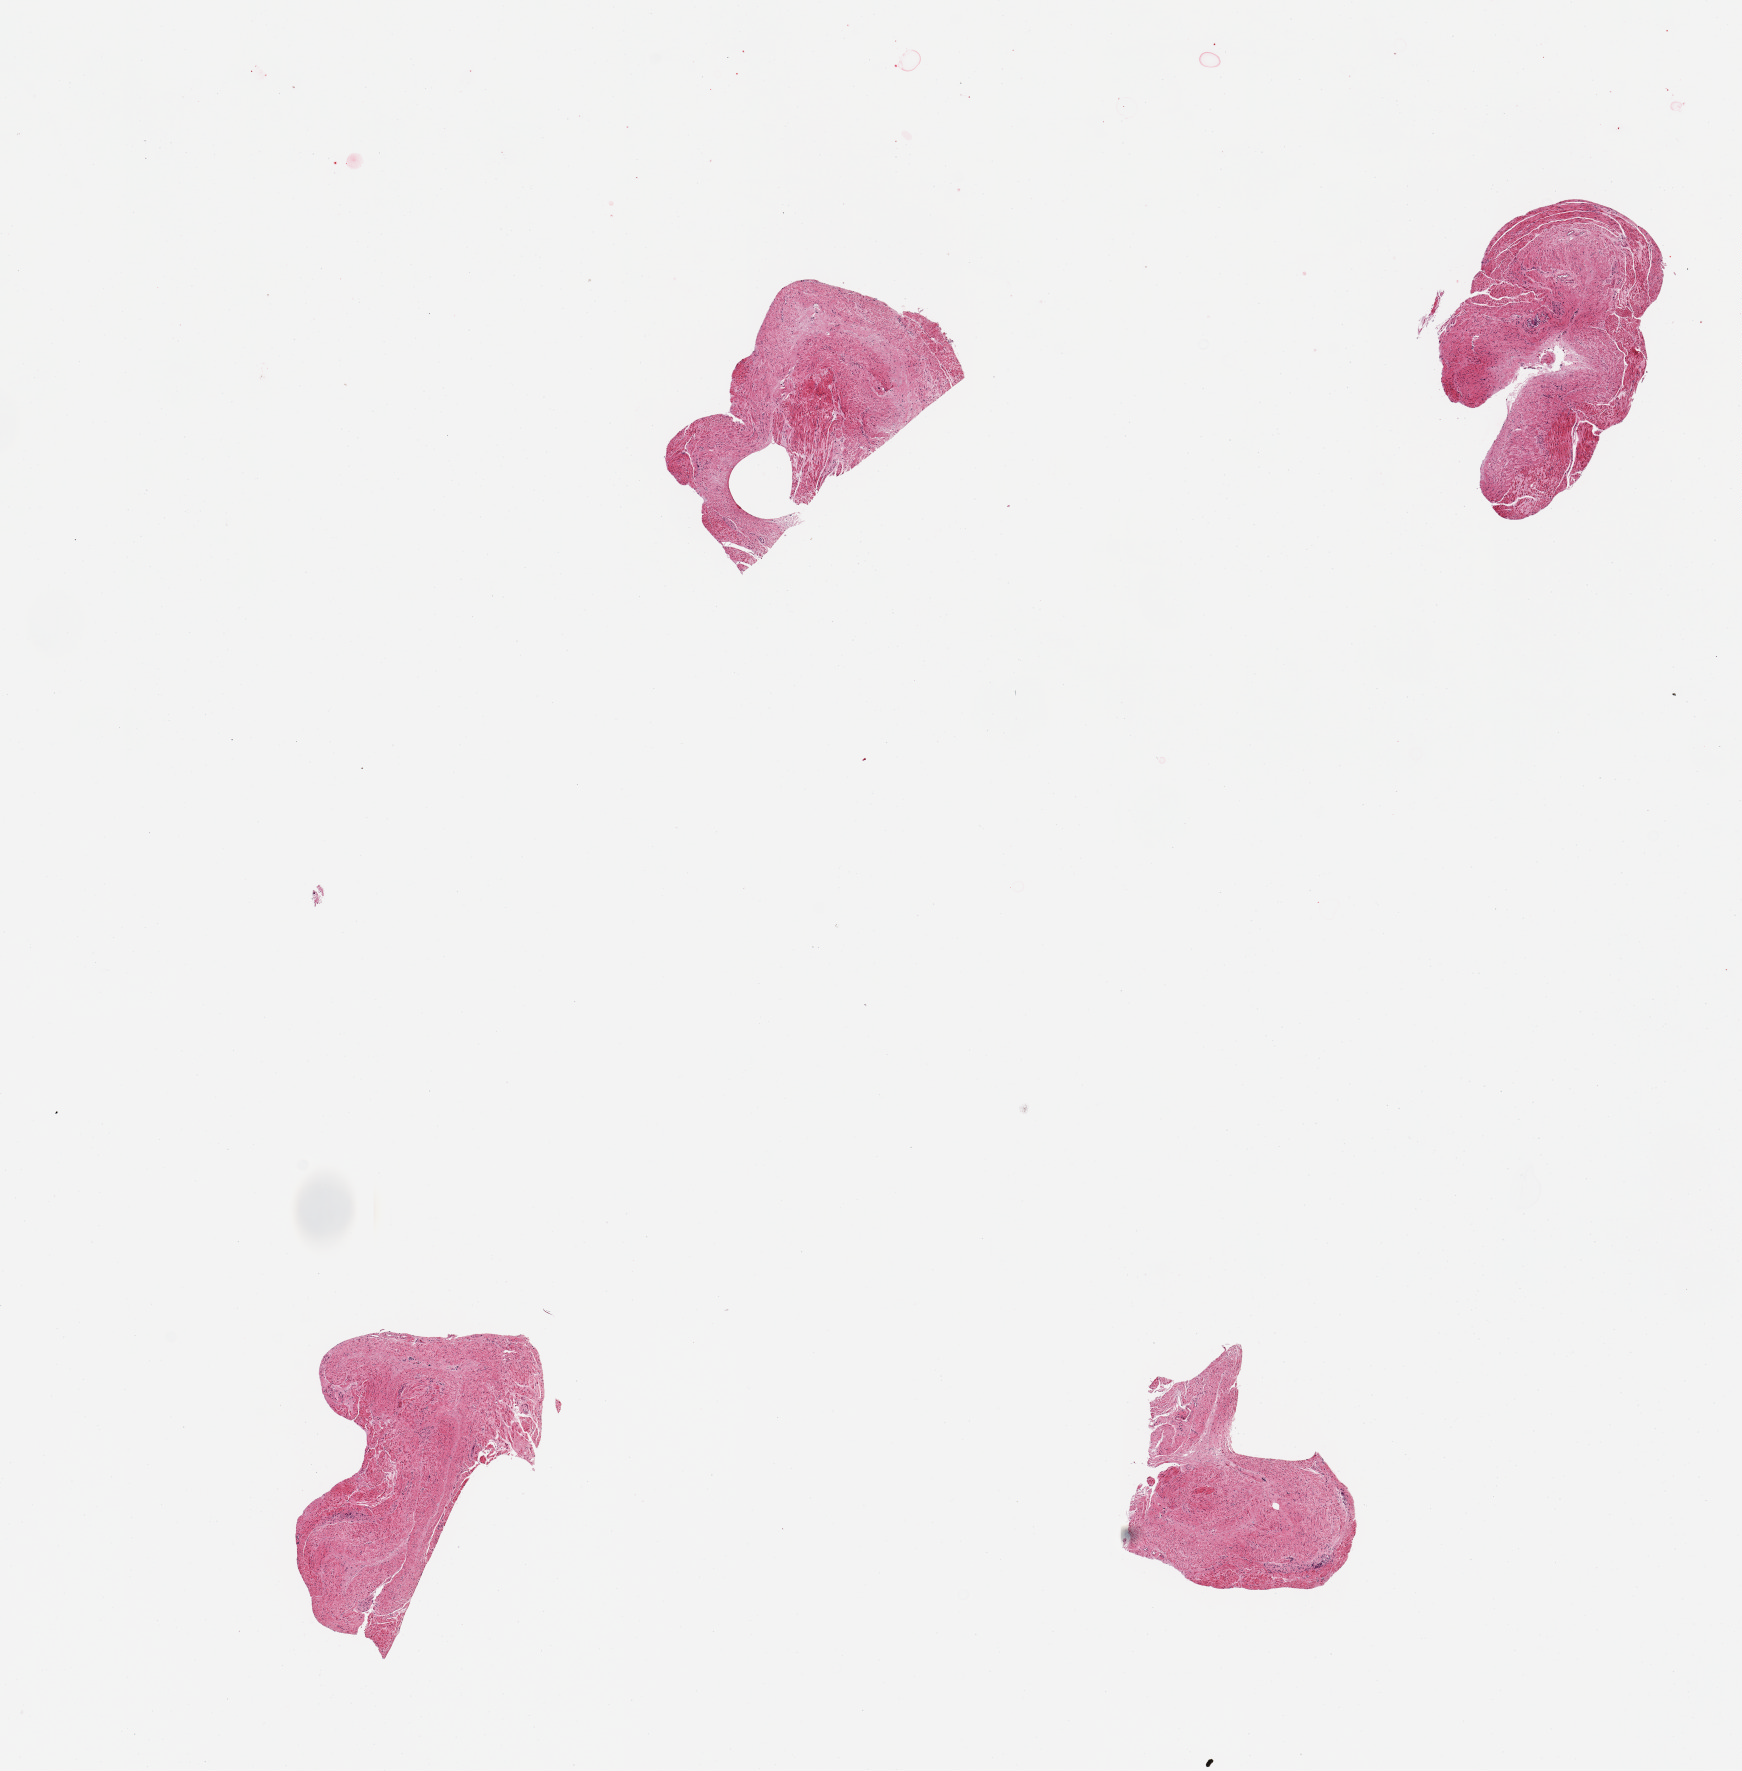
Digitized hematoxylin and eosin (H&E)-stained section, whole scanned area (about 13.8 x 14.0 mm, slide scanned at 20x) shown as a low-resolution overview. PAXgene-fixed, paraffin-embedded tissue. Sampled site (target tissue): stomach. Donor tissue sample. Donor: female.
Review note (as recorded): 4 pieces; muscularis only.